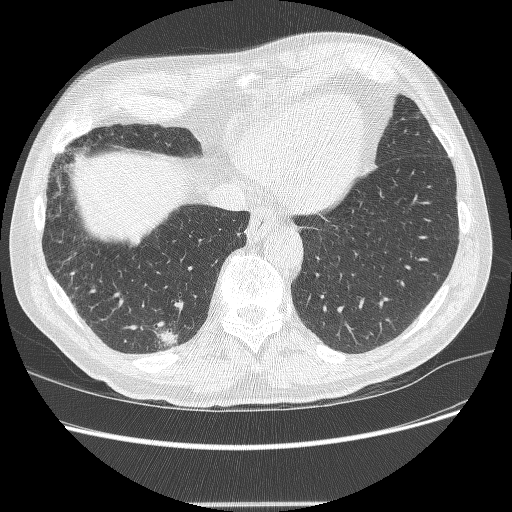
Low-dose screening chest CT, axial slice. Second annual screen. Lung window (W 1500 / L -600 HU). 1.25 mm slice thickness. Slice 59 of 245 in the series. Male, age 71 years at enrolment. Current smoker at enrolment.
- Expert-annotated lung lesion, bounding box (x1, y1, x2, y2) in pixels: (137, 321, 187, 359).
- The screening reader recorded 5 non-calcified nodules or masses ≥4 mm on this exam (right lower lobe, right lower lobe, right upper lobe, right upper lobe, right upper lobe); which of them this box marks is not recorded.